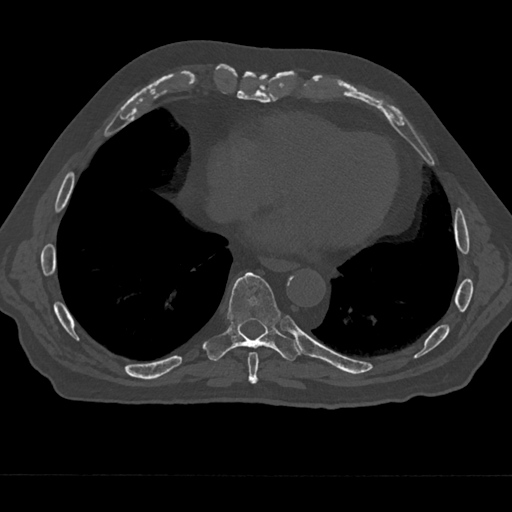
CT including the spine, one axial slice; position 274 of 797 along the scan axis; reconstruction kernel Br40s/3; bone window (W 1800 / L 400 HU); 0.5 mm slice thickness; 512 × 512 image matrix, field of view 377 × 377 mm. Patient: male, 75 years. From the clinical record (not read from this slice): primary cancer: renal; vertebrae with lytic lesions (as recorded): T4.
Outlined on this slice (semi-automatically segmented with operator editing):
- T8 vertebra: bounding box (x1, y1, x2, y2) in pixels: (248, 352, 259, 384)
- T9 vertebra: (203, 272, 300, 361)